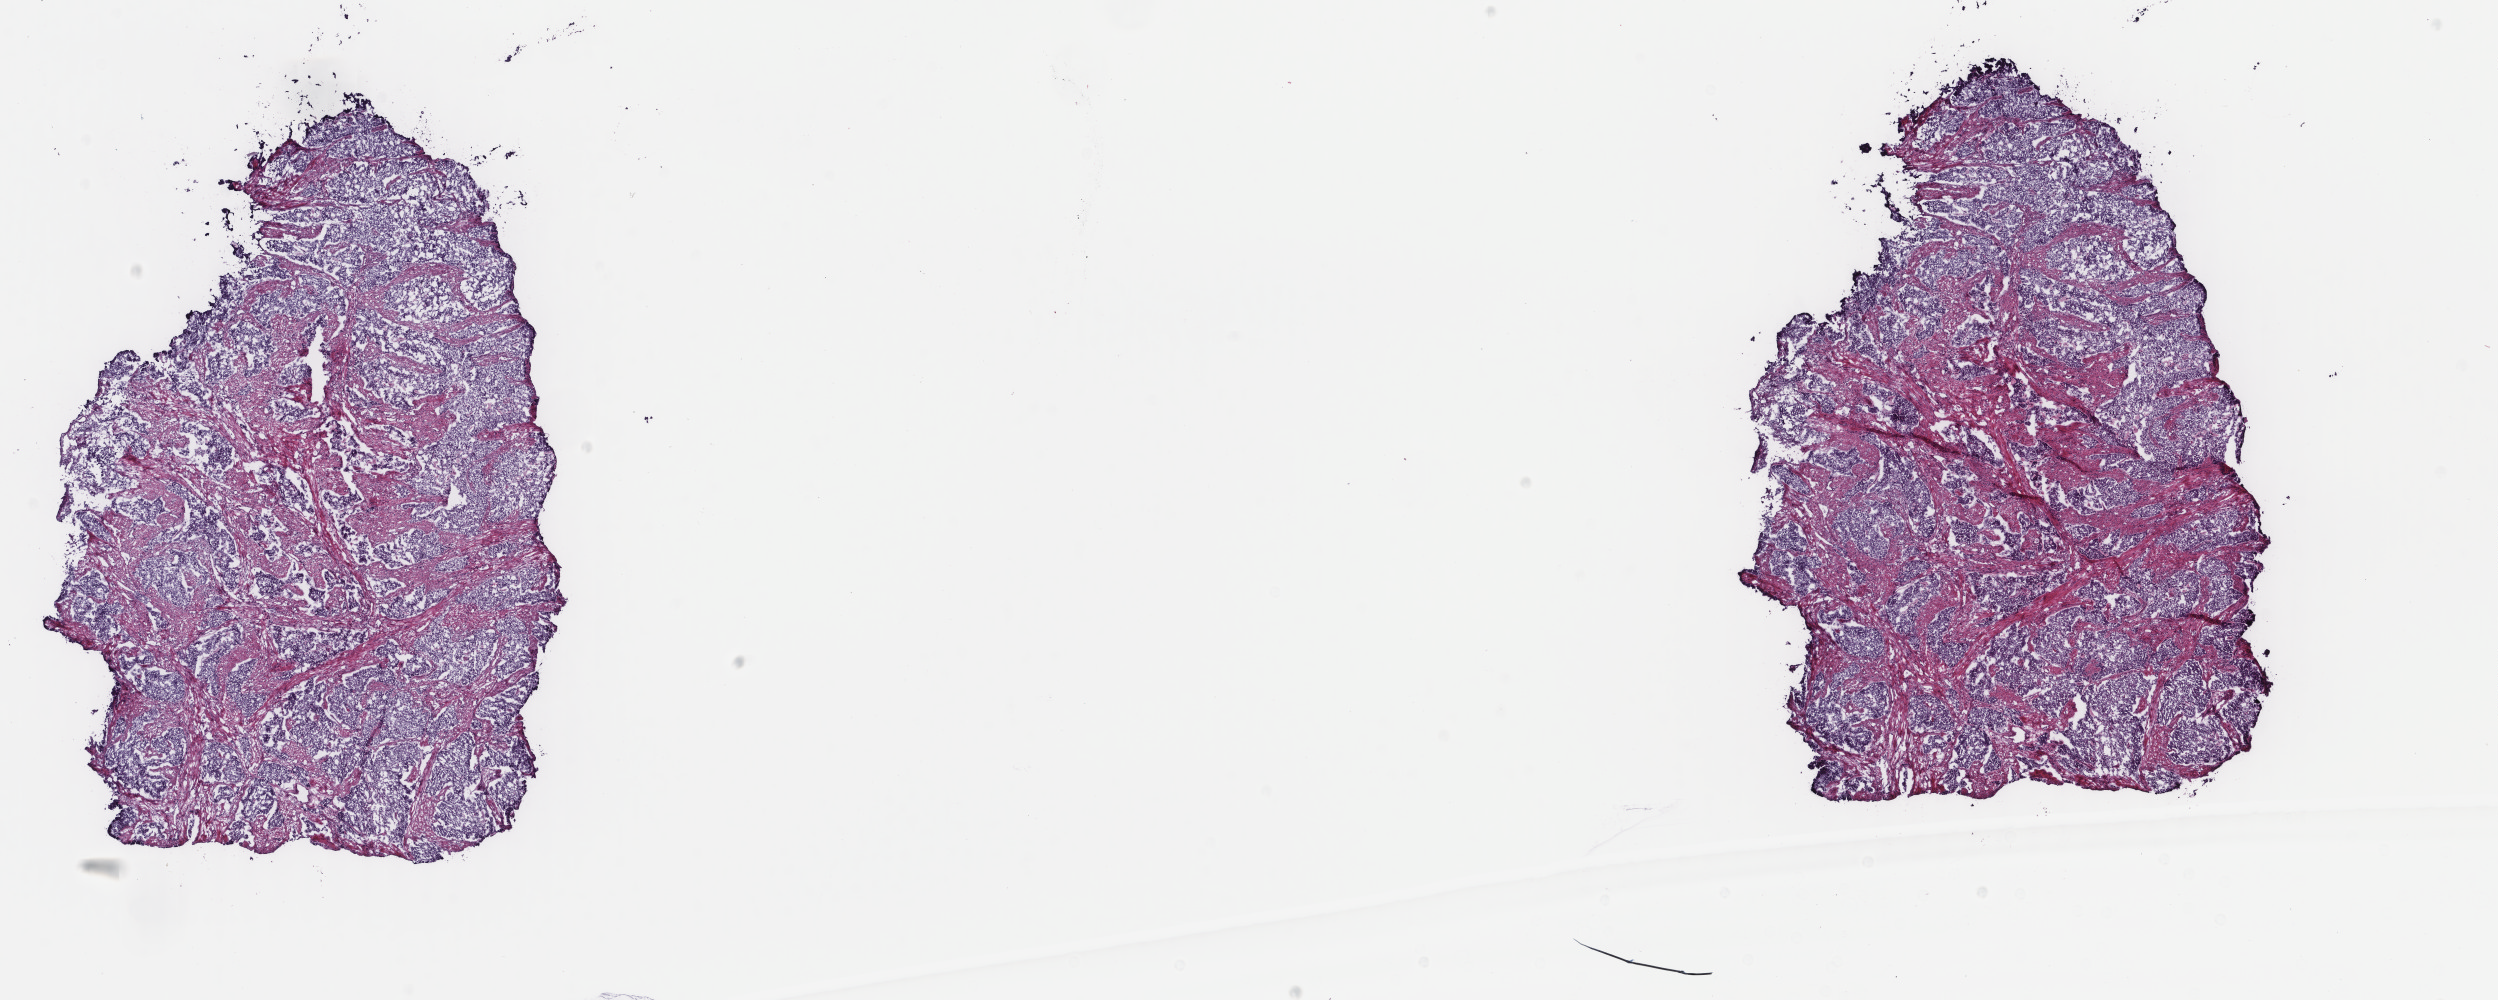
Whole-slide histology image, H&E — shown as a low-resolution overview of the whole scanned area (about 19.8 x 7.9 mm, from a 40x scan). Frozen section. Sample: primary tumour, uterus. Female patient; age at initial diagnosis 76 years. Histologic grade: G3 (poorly differentiated). Slide review estimates, as recorded: tumour cells 60%, tumour nuclei 60%, normal cells 0%, stromal cells 30%, necrosis 10%. Infiltration values recorded for this section: lymphocyte infiltration 40%, monocyte infiltration 20%, neutrophil infiltration 20%.
FIGO stage: IB. Lymph nodes positive (case pathology): 0 of 29 examined. Histologic diagnosis: Endometrioid adenocarcinoma, NOS (endometrium).